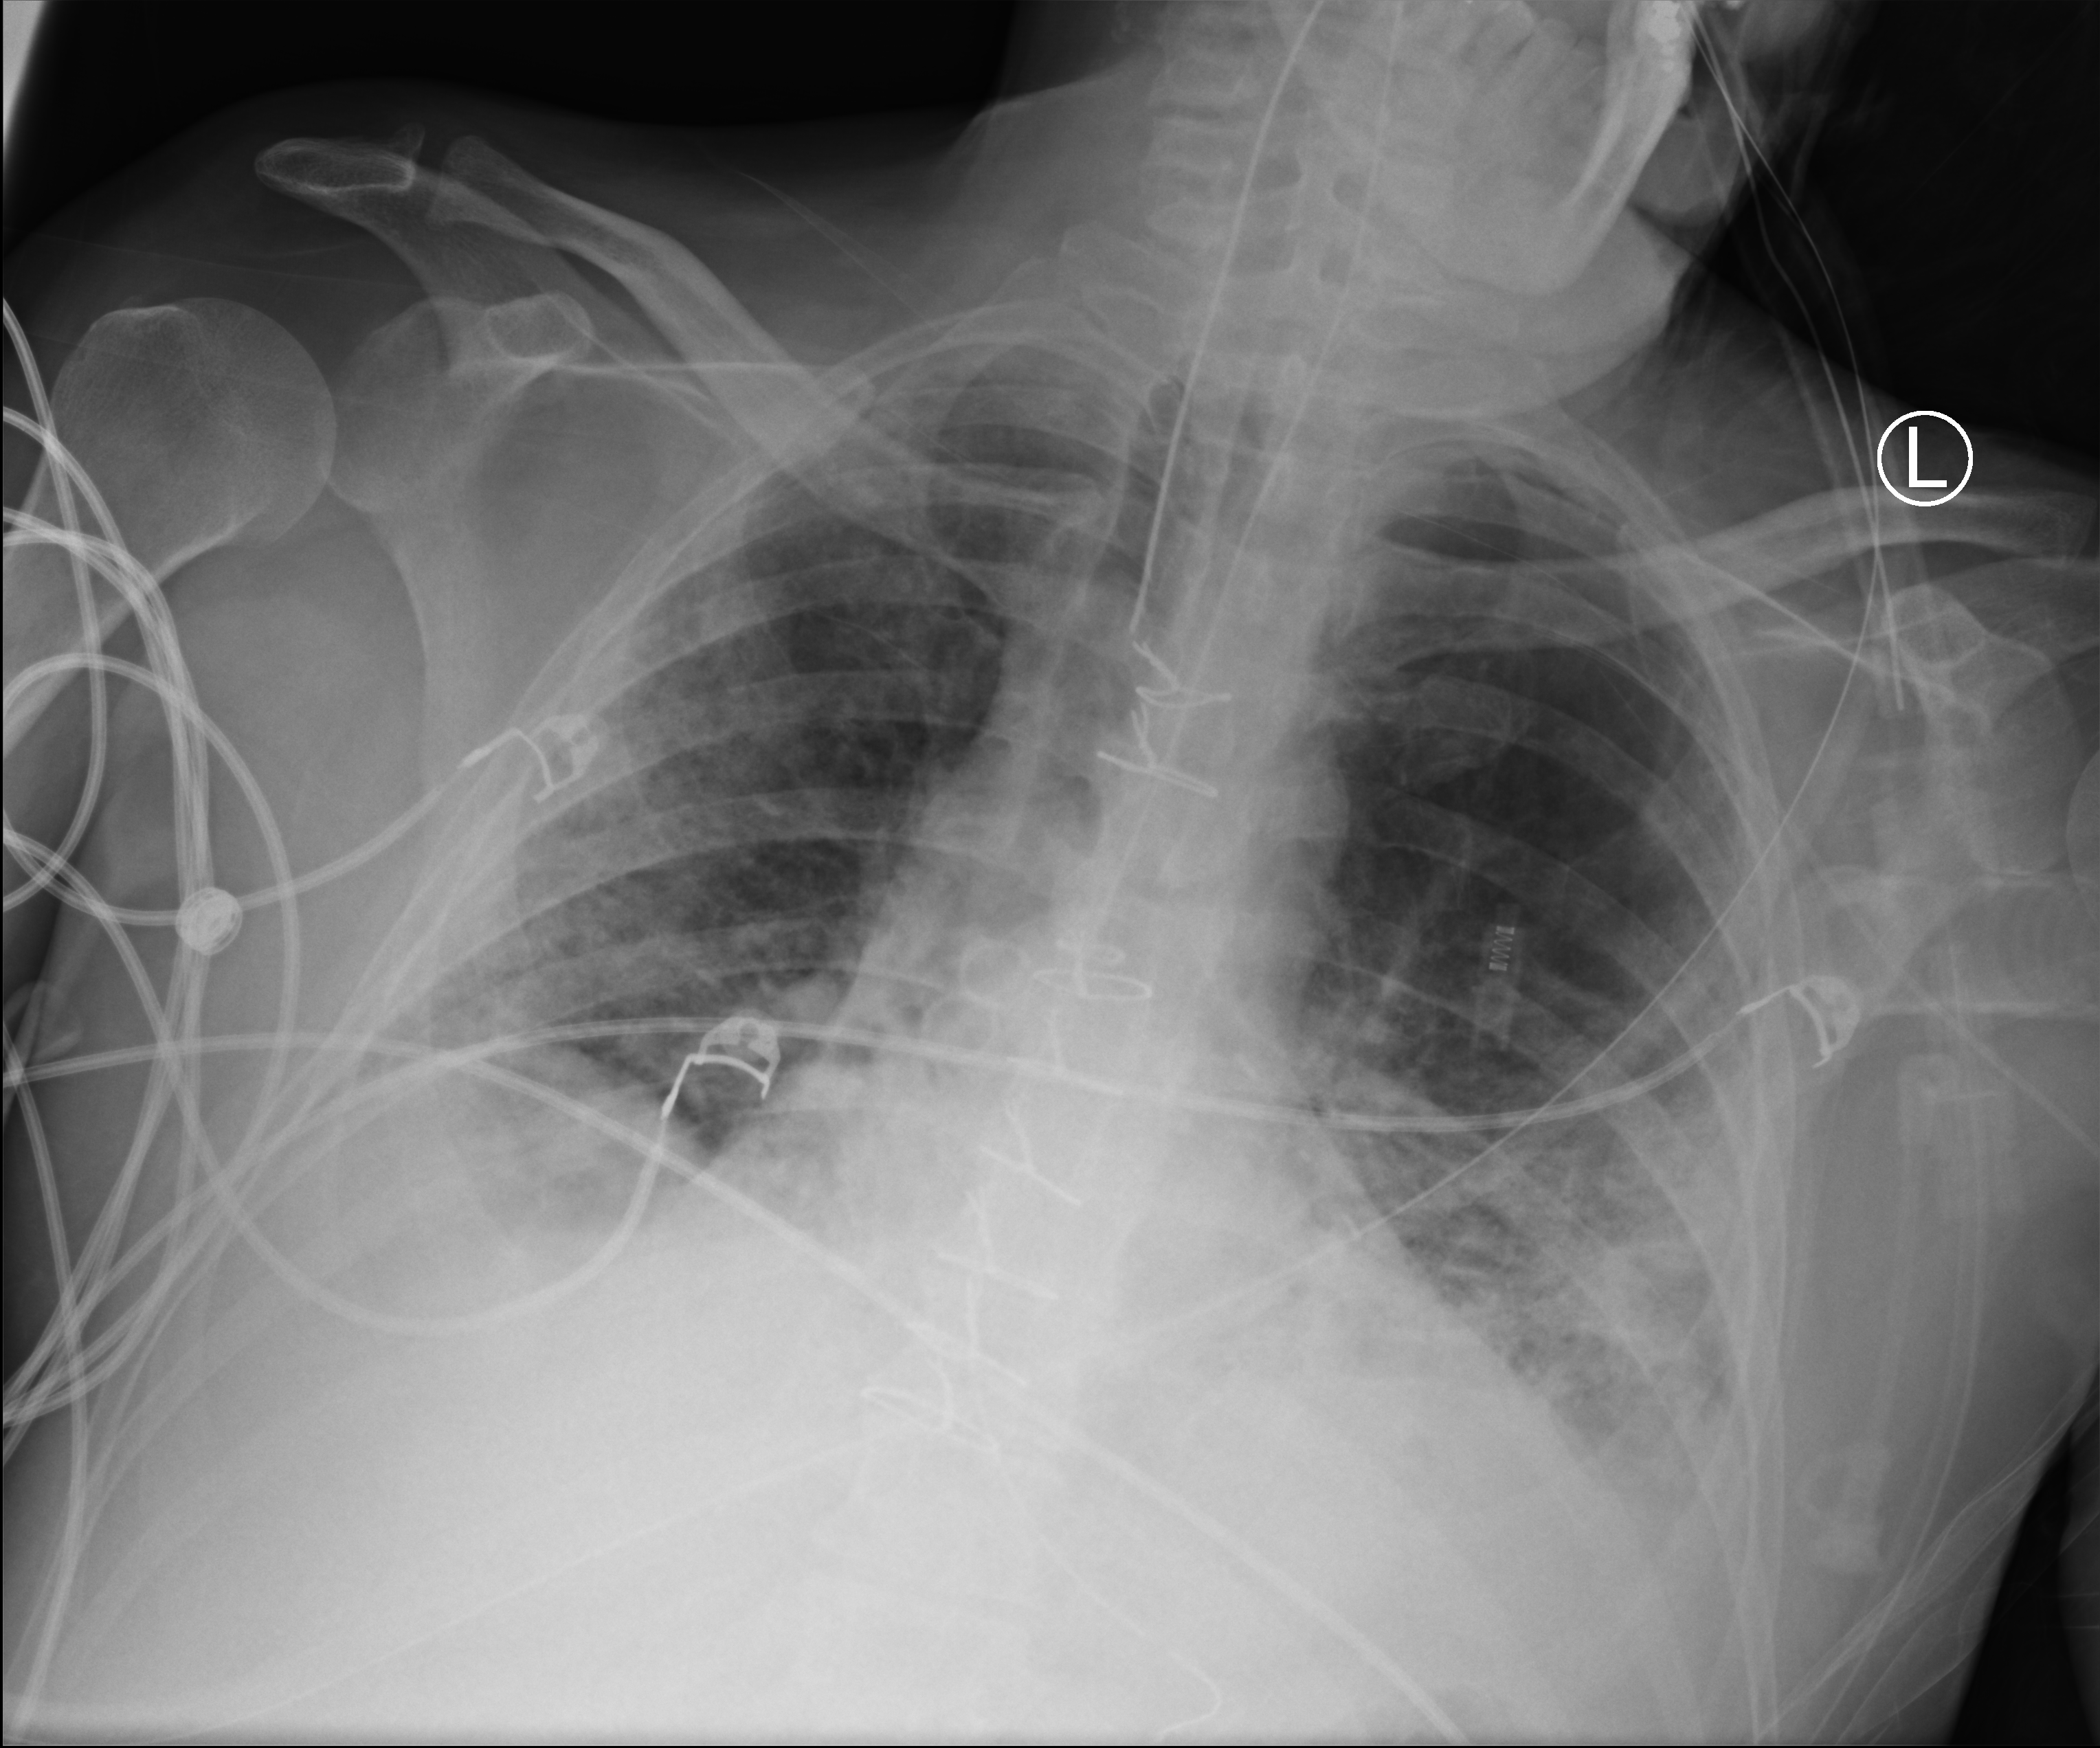
Chest X-ray (portable), anteroposterior (AP) projection. Male patient hospitalised with COVID-19, age 18–59 years.
Hospital-stay facts (about this admission, not read from this image; timing relative to this image not recorded):
- mechanically ventilated during this hospital stay: yes